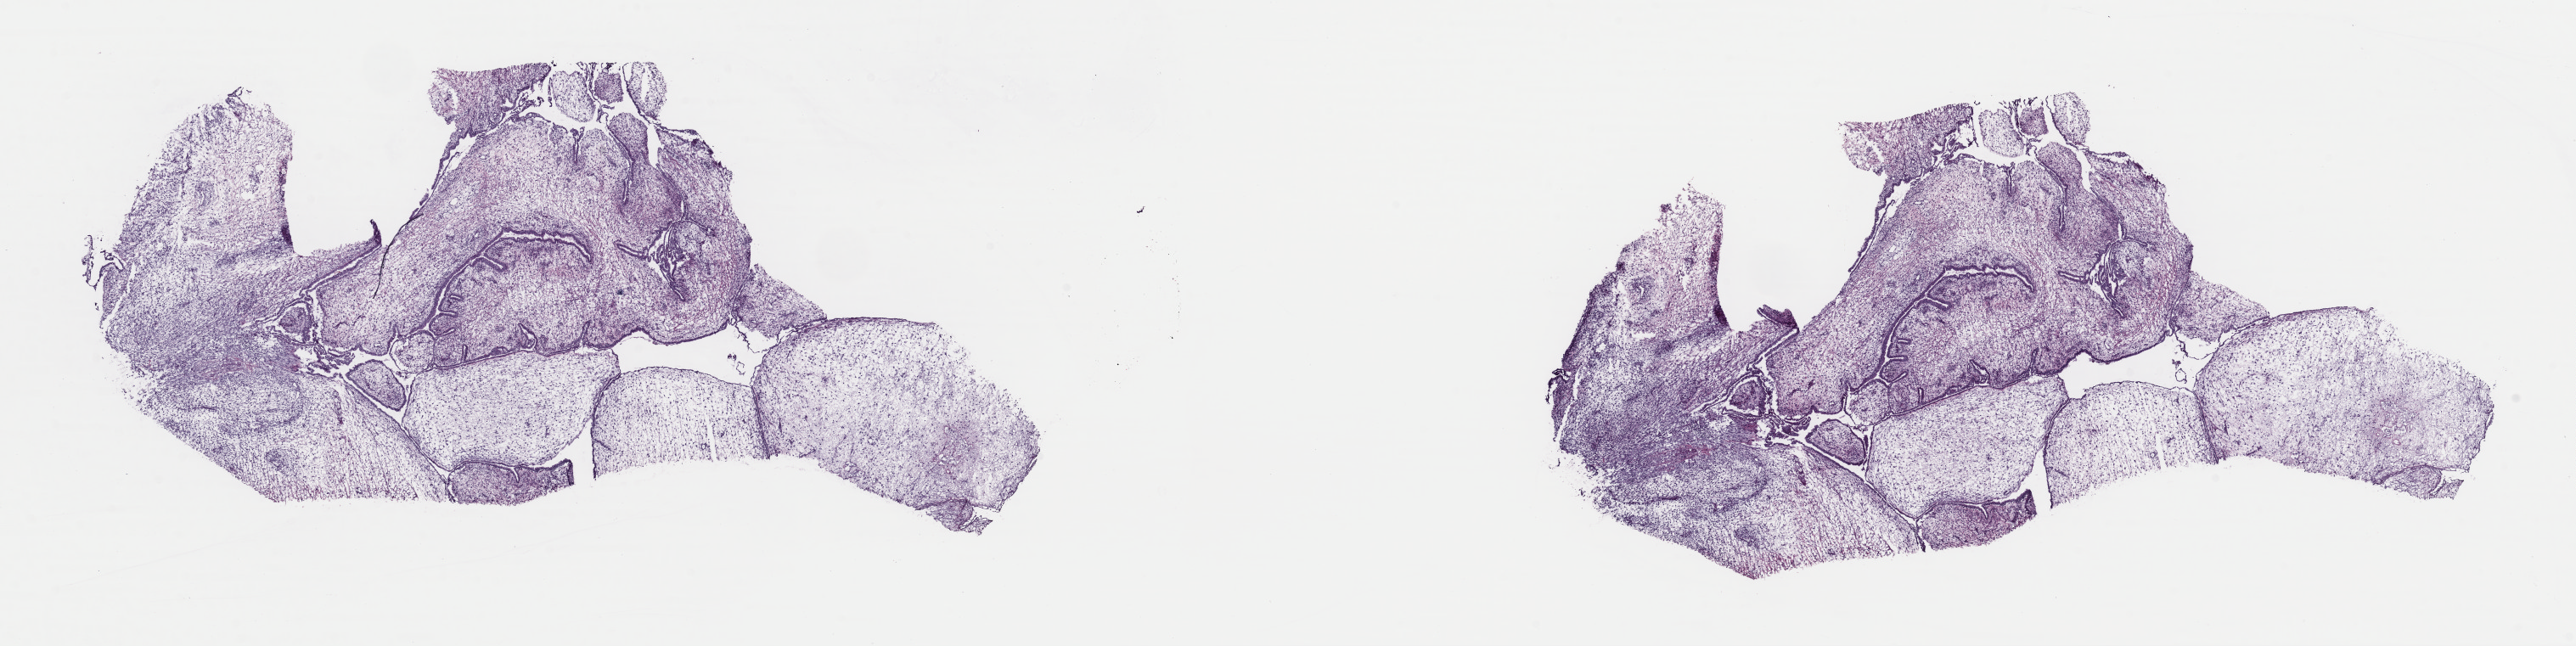
H&E whole-slide image, a low-resolution overview of the entire scanned area, about 24.0 x 6.0 mm; frozen section from the top of the tissue portion; sample: primary tumour, breast. Patient: female, age at initial diagnosis 88 years. Slide review estimates, as recorded: tumour cells 100%, tumour nuclei 80%, normal cells 0%, stromal cells 0%, necrosis 0%. Infiltration values recorded for this section: lymphocyte infiltration 1%, monocyte infiltration 0%, neutrophil infiltration 0%.
Laterality: right. TNM: T1c N1mi MX. Pathologic diagnosis: Phyllodes tumor, malignant. AJCC pathologic stage: IB (7th edition).